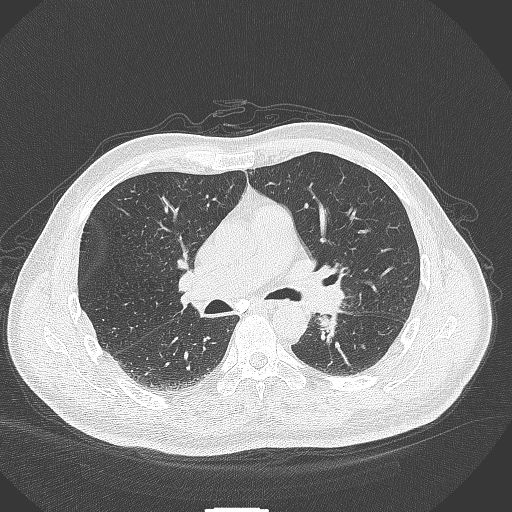
Chest CT, one axial slice. Position 244 of 429 along the scan axis. Lung window (W 1500 / L -600 HU). 1 mm slice thickness. 512 × 512 image matrix, field of view 400 × 400 mm. Male patient, age 55 years. Case-level facts recorded for this patient, not image findings: clinical TNM (as recorded): T3 N0 M1c; histopathological grade: G3.
Outlined on this slice (rectangle marked by the reading radiologist):
- lung tumour (recorded histology: adenocarcinoma): bounding box (x1, y1, x2, y2) in pixels: (312, 308, 341, 340)